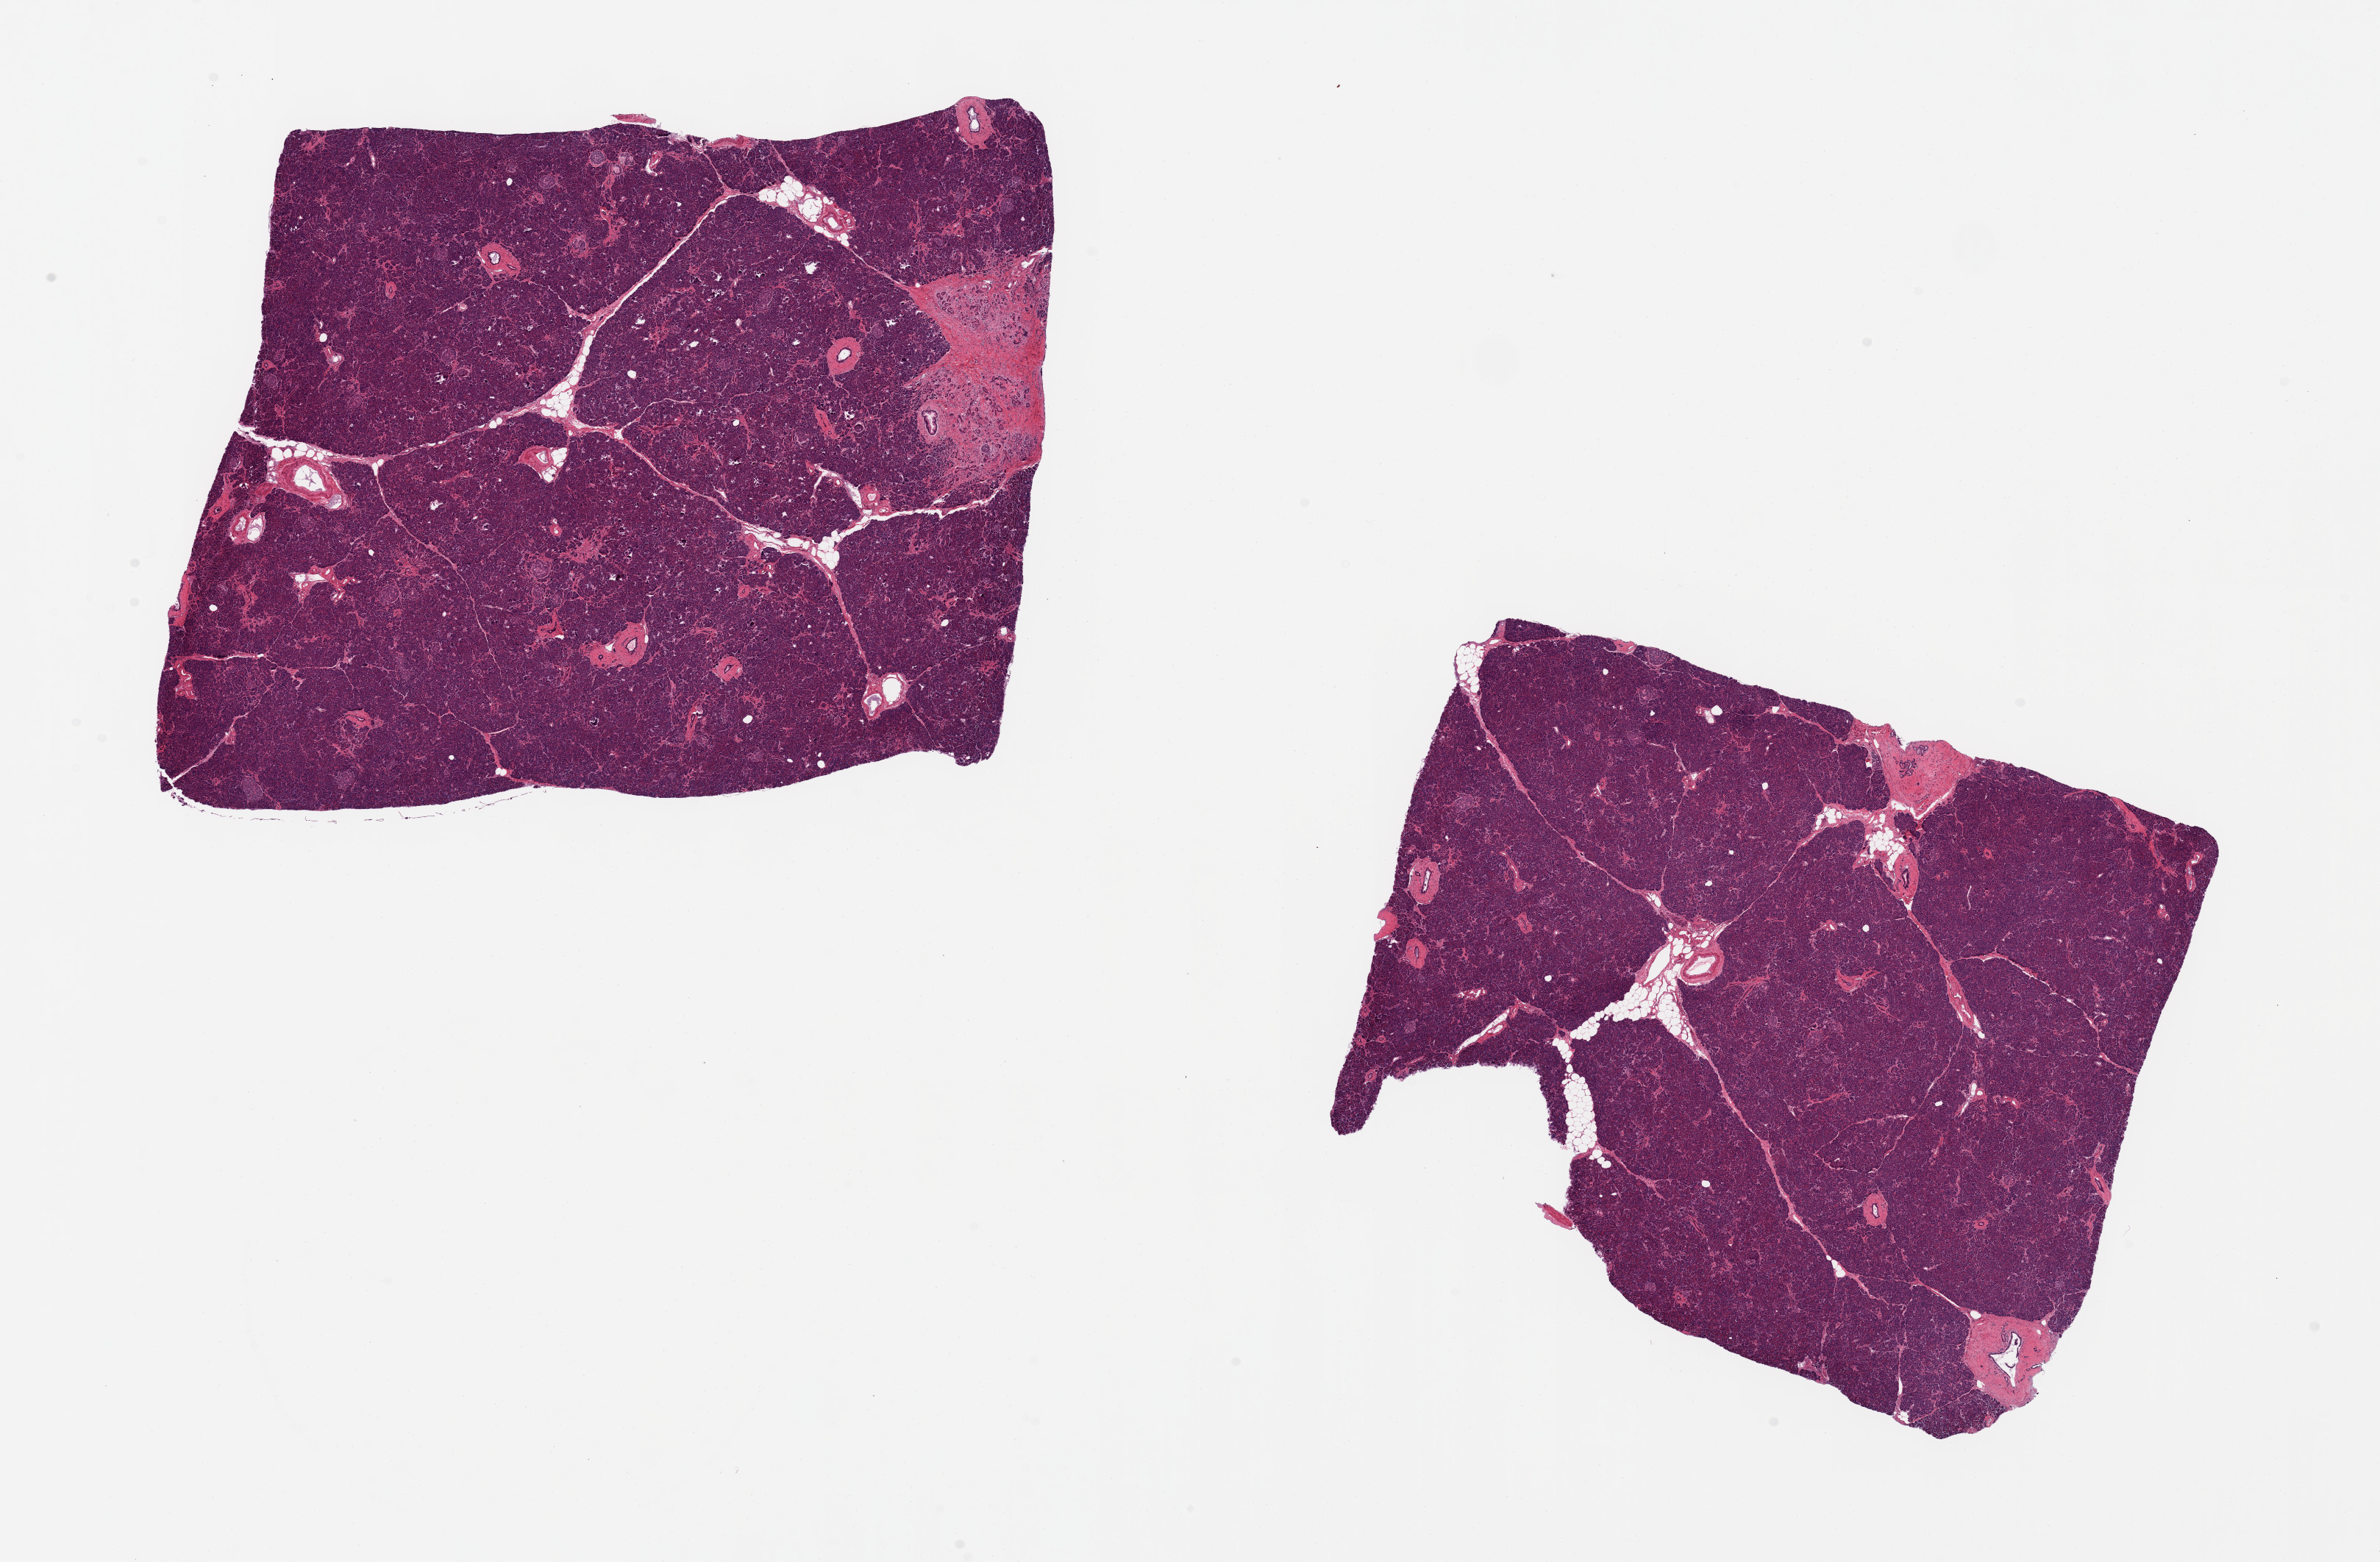
Whole-slide image, H&E stain — shown as a low-resolution overview of the whole scanned area (about 25.6 x 16.8 mm), PAXgene-fixed, paraffin-embedded tissue, target tissue: pancreas, donor tissue sample. Donor sex: male.
Reviewer comment on this tissue sample: 2 ~7x8mm pieces, well preserved. Islets well represented.